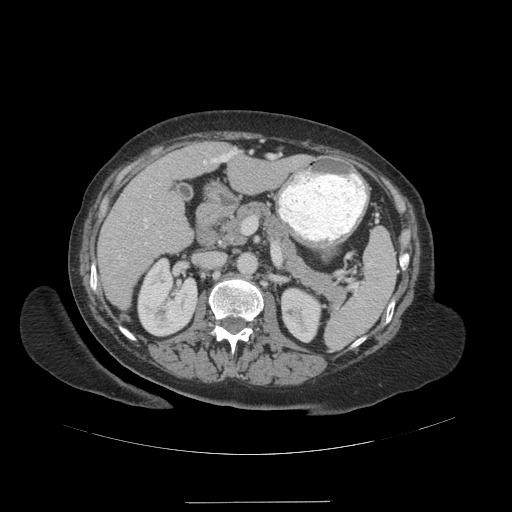
Contrast-enhanced abdominal CT (liver protocol), one axial slice. Reconstruction kernel STANDARD. 140 kVp. Soft-tissue window (W 400 / L 40 HU). 2.5 mm slice thickness. 512 × 512 image matrix, field of view 440 × 440 mm. Case-level facts recorded for this patient, not image findings: diagnosis: hepatocellular carcinoma (patient treated with transarterial chemoembolisation; whether this scan precedes or follows treatment is not stated here); TNM stage (as recorded): Stage-IVA; Child-Pugh class: A; tumour nodularity: multinodular.
Annotated regions visible in this slice (semi-automatically segmented with operator editing):
- liver parenchyma outside the tumour (the mass and vessels are separate outlines, so this box may not span the whole liver): box from (x=98, y=141) to (x=306, y=309) px
- liver vessels: (x=118, y=149)–(x=238, y=259)